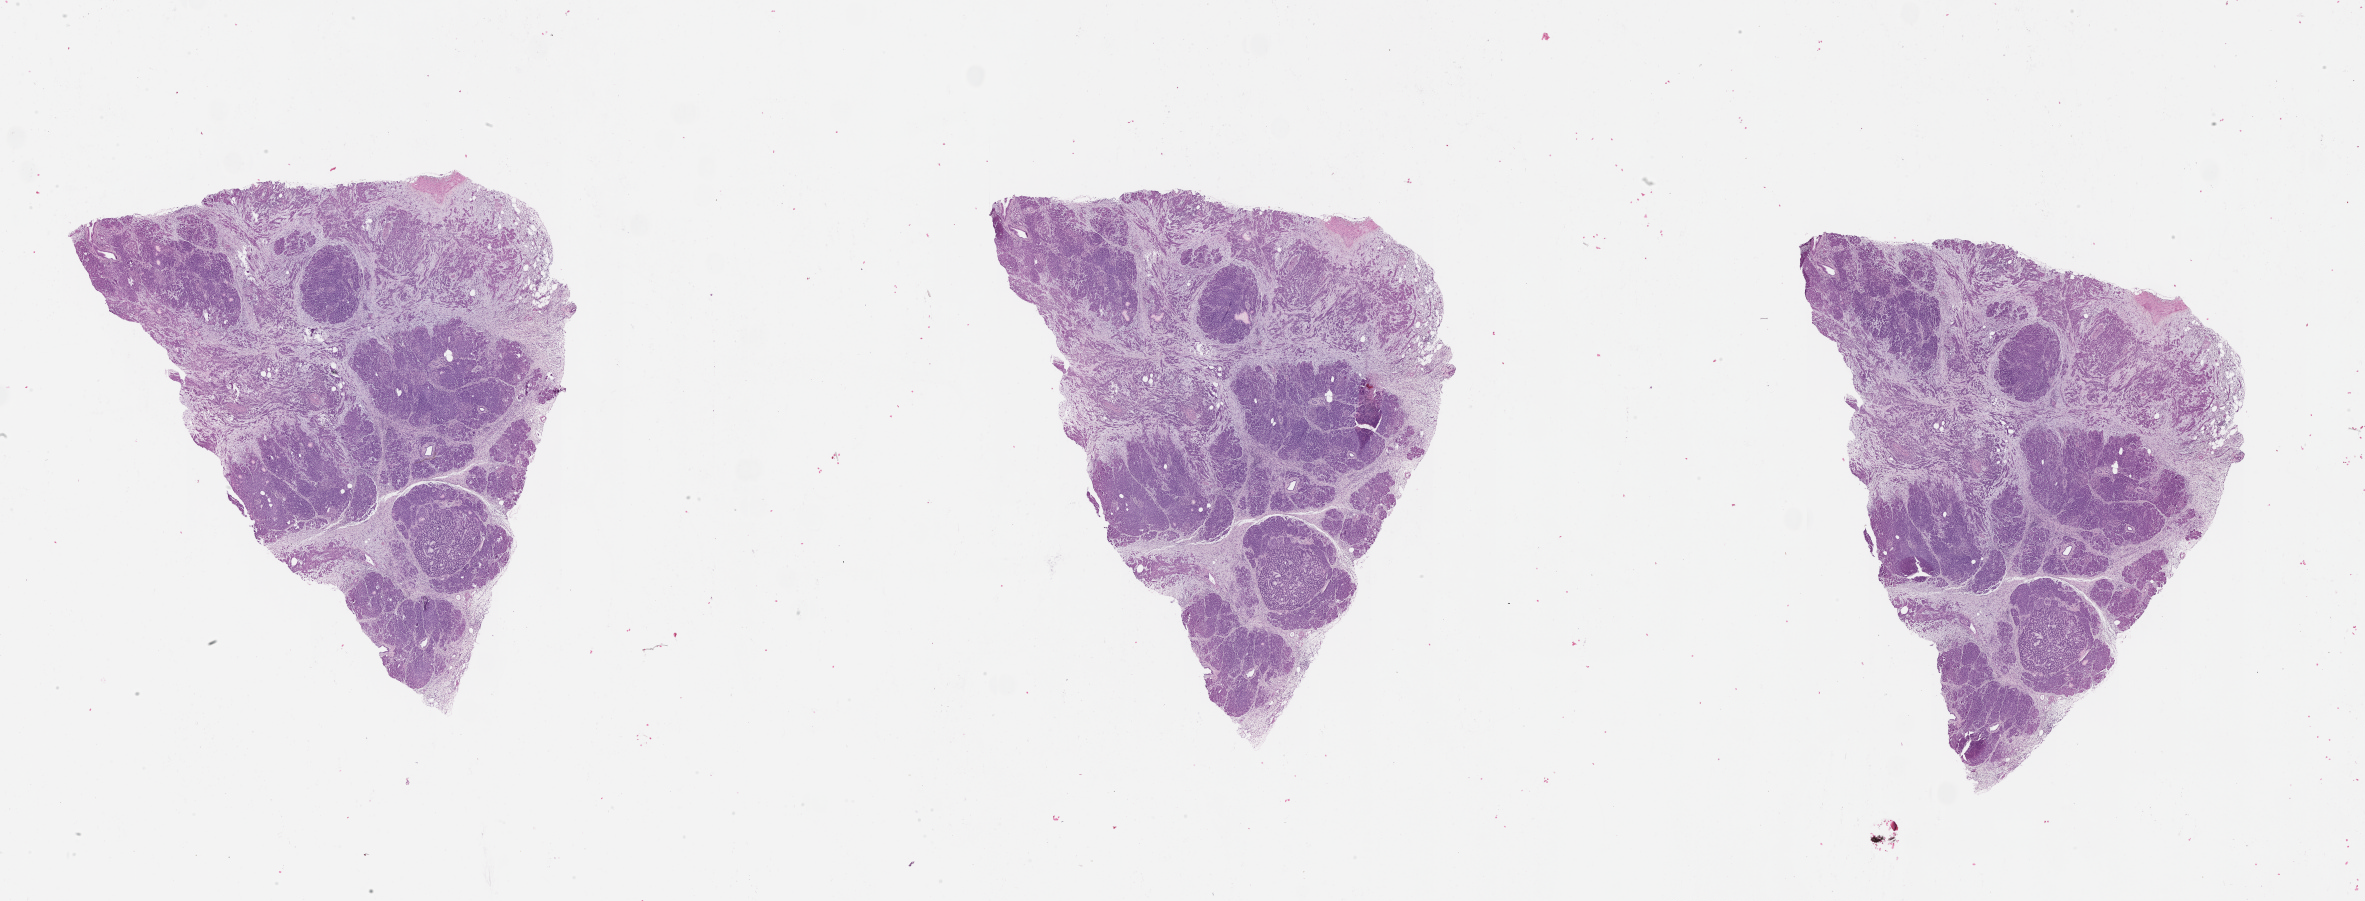
Digitized H&E-stained tissue section (whole slide), whole scanned area (about 38.1 x 14.5 mm) shown as a low-resolution overview; normal (non-tumour) tissue sample, sampled site: pancreas. Female, 66 y/o.
This section: normal (non-tumour) tissue from the same patient. Patient diagnosis: Infiltrating duct carcinoma, NOS.